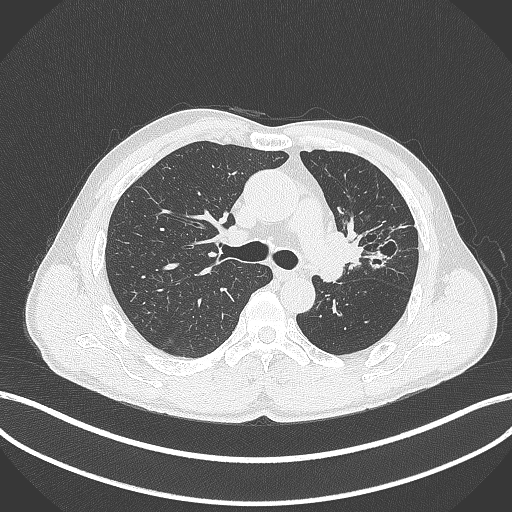
Chest CT, one axial slice. Reconstruction kernel B70f. Lung window (W 1500 / L -600 HU). 1 mm slice thickness. 512 × 512 image matrix, field of view 400 × 400 mm. Patient: male, 57 years. Case-level facts recorded for this patient, not image findings: clinical TNM (as recorded): T2b N0 M0.
Annotated regions visible in this slice (rectangle marked by the reading radiologist):
- lung tumour (recorded histology: squamous cell carcinoma): bounding box [x1, y1, x2, y2] px = [322, 225, 364, 269]